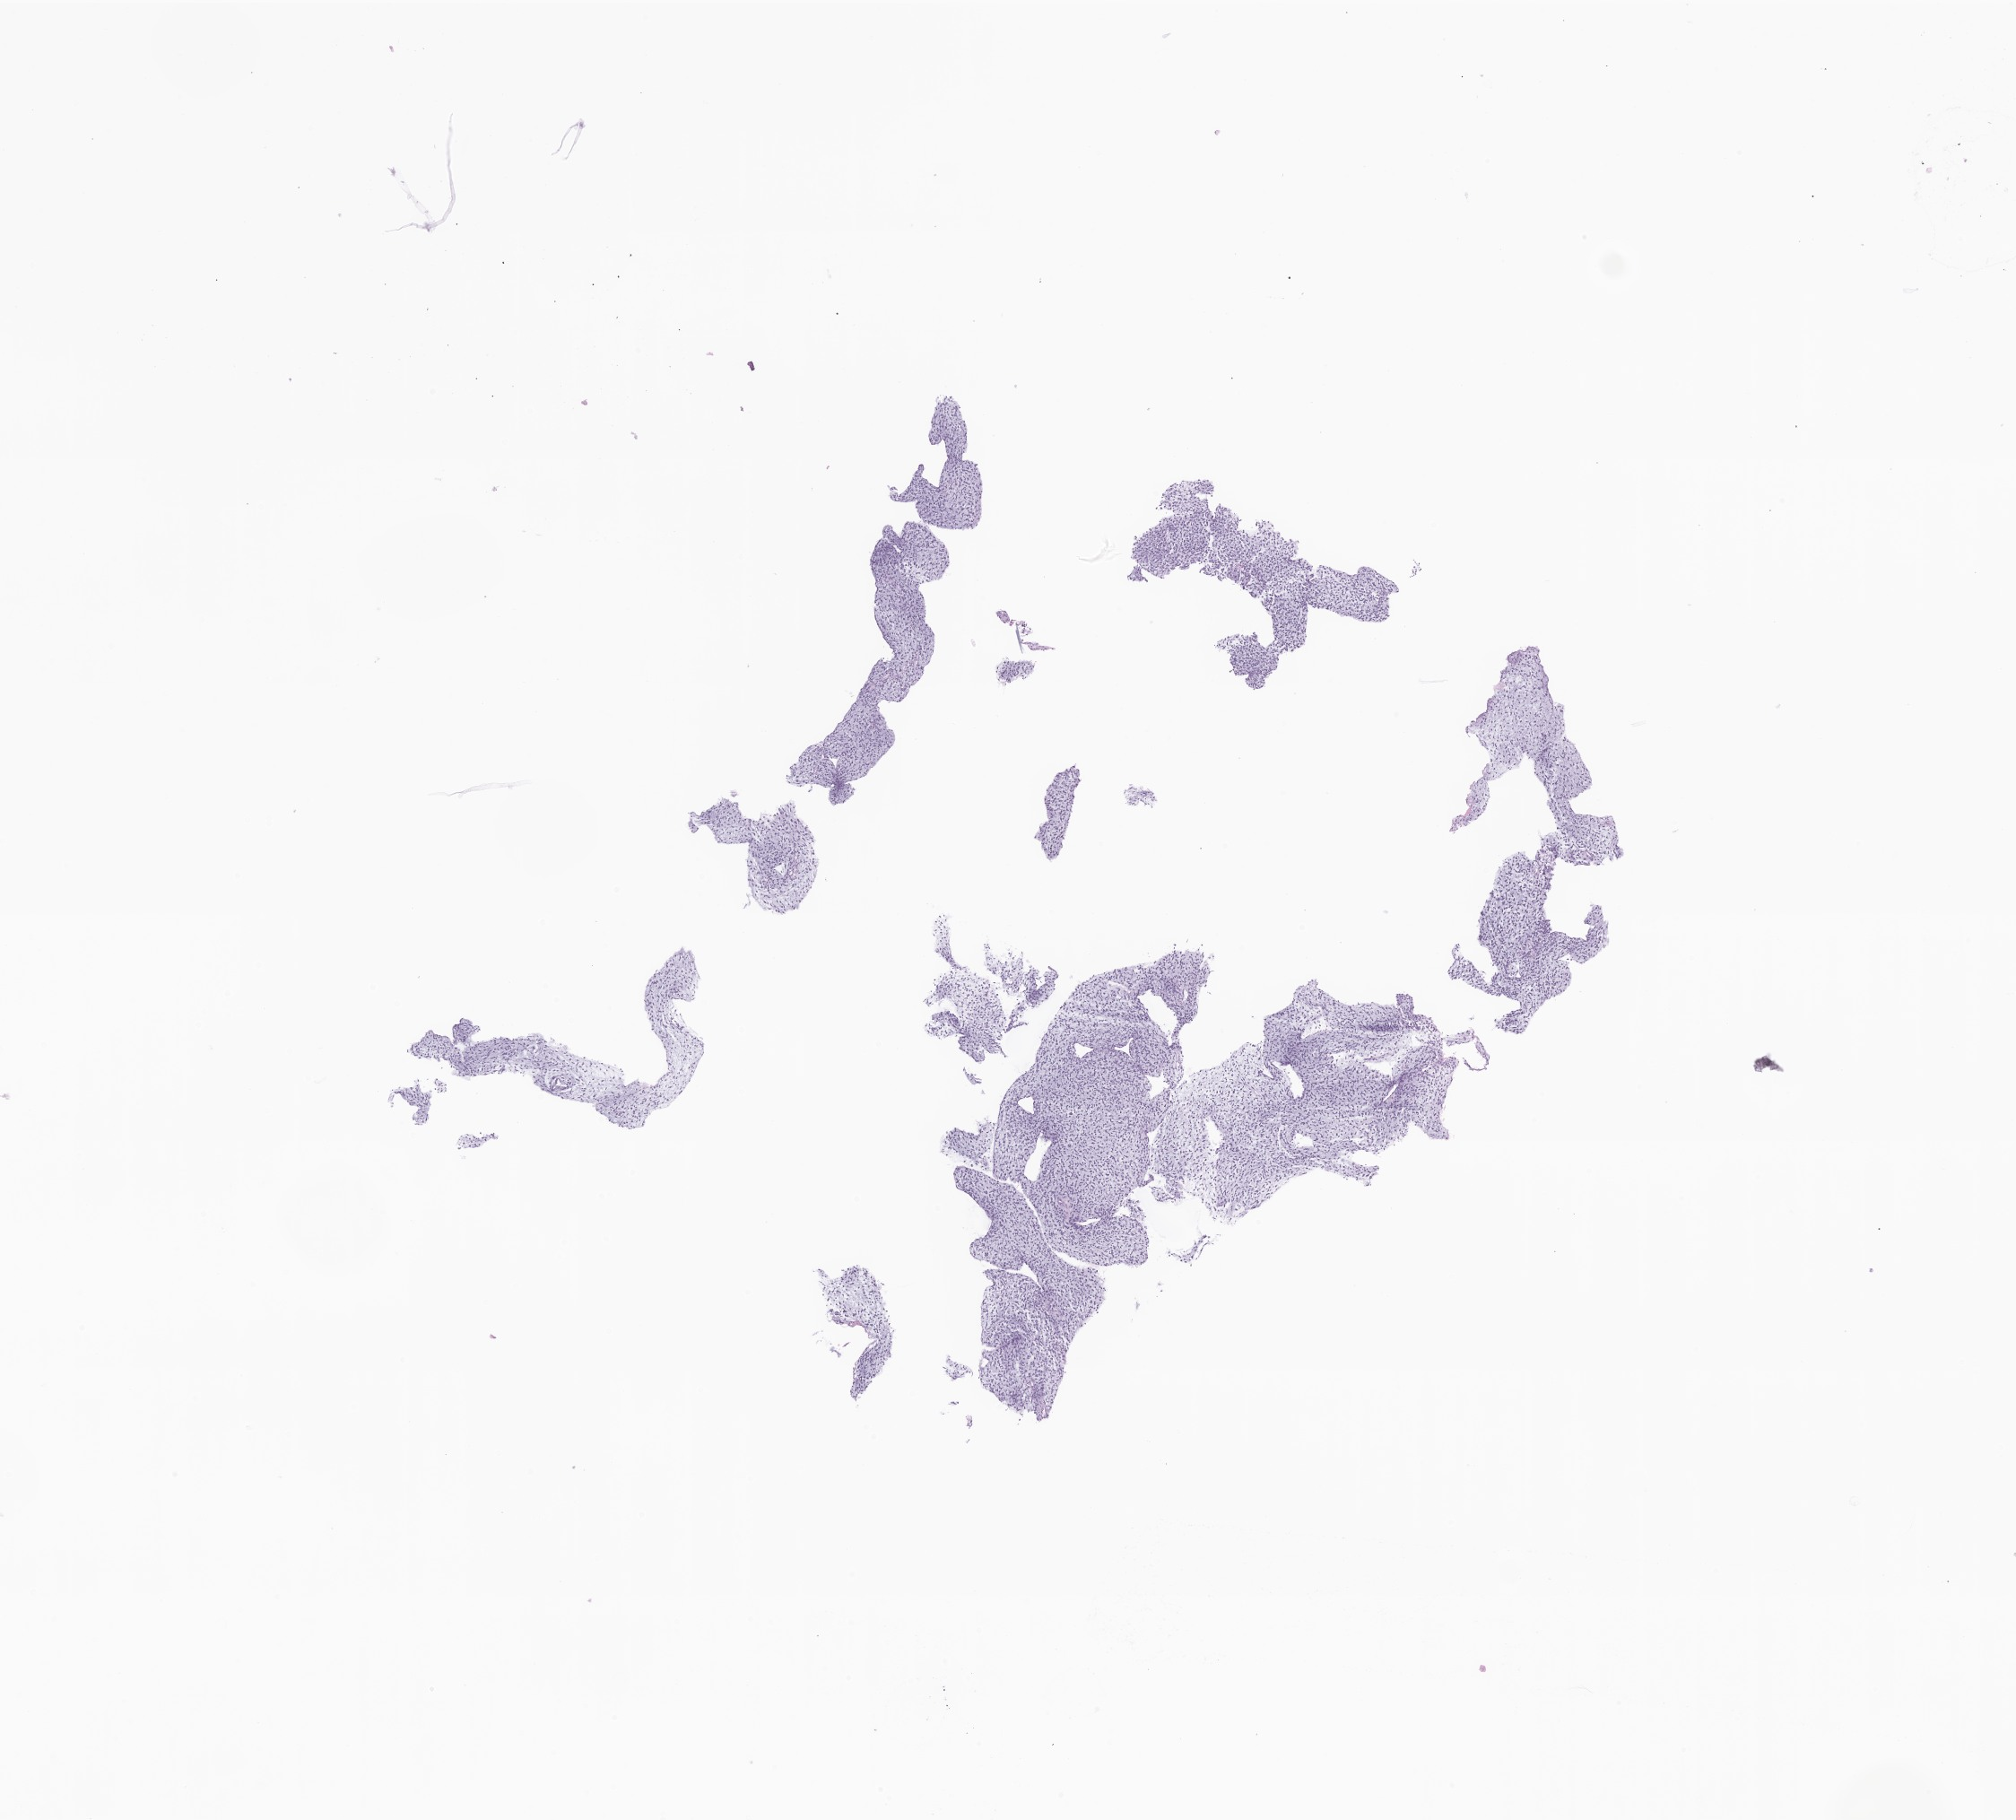
Haematoxylin and eosin whole-slide image of tumor tissue from the maxillary sinus — low-resolution overview of the scanned area, about 9.5 x 8.6 mm. Formalin-fixed, paraffin-embedded (FFPE) tissue. Patient female; age 35 months.
* recorded diagnosis: Embryonal rhabdomyosarcoma, NOS